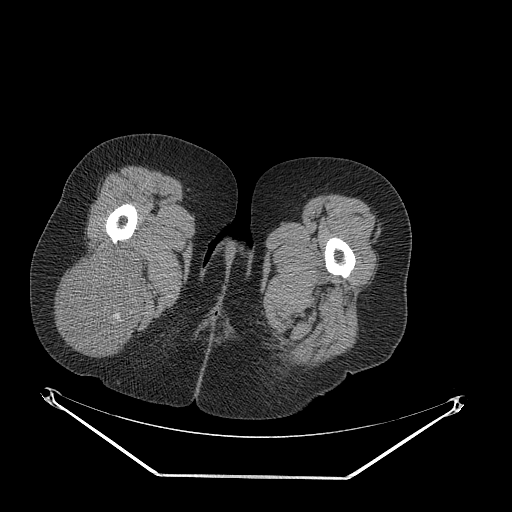
CT of an extremity soft-tissue mass (from a PET/CT study), one axial slice; slice 45 of 257 in the series (ordered by position); reconstruction kernel STANDARD; 140 kVp; soft-tissue window (W 400 / L 40 HU); 3.75 mm slice thickness; 512 × 512 image matrix. Female patient. Case-level facts recorded for this patient, not image findings: histological type: synovial sarcoma; grade: intermediate; site of the primary tumour: right buttock.
Outlined on this slice (expert contour drawn on MRI and transferred to this co-registered scan by the dataset authors):
- gross tumour volume including surrounding oedema: bounding box (x1, y1, x2, y2) in pixels: (62, 247, 147, 350)
- gross tumour volume (mass): (62, 247, 147, 350)